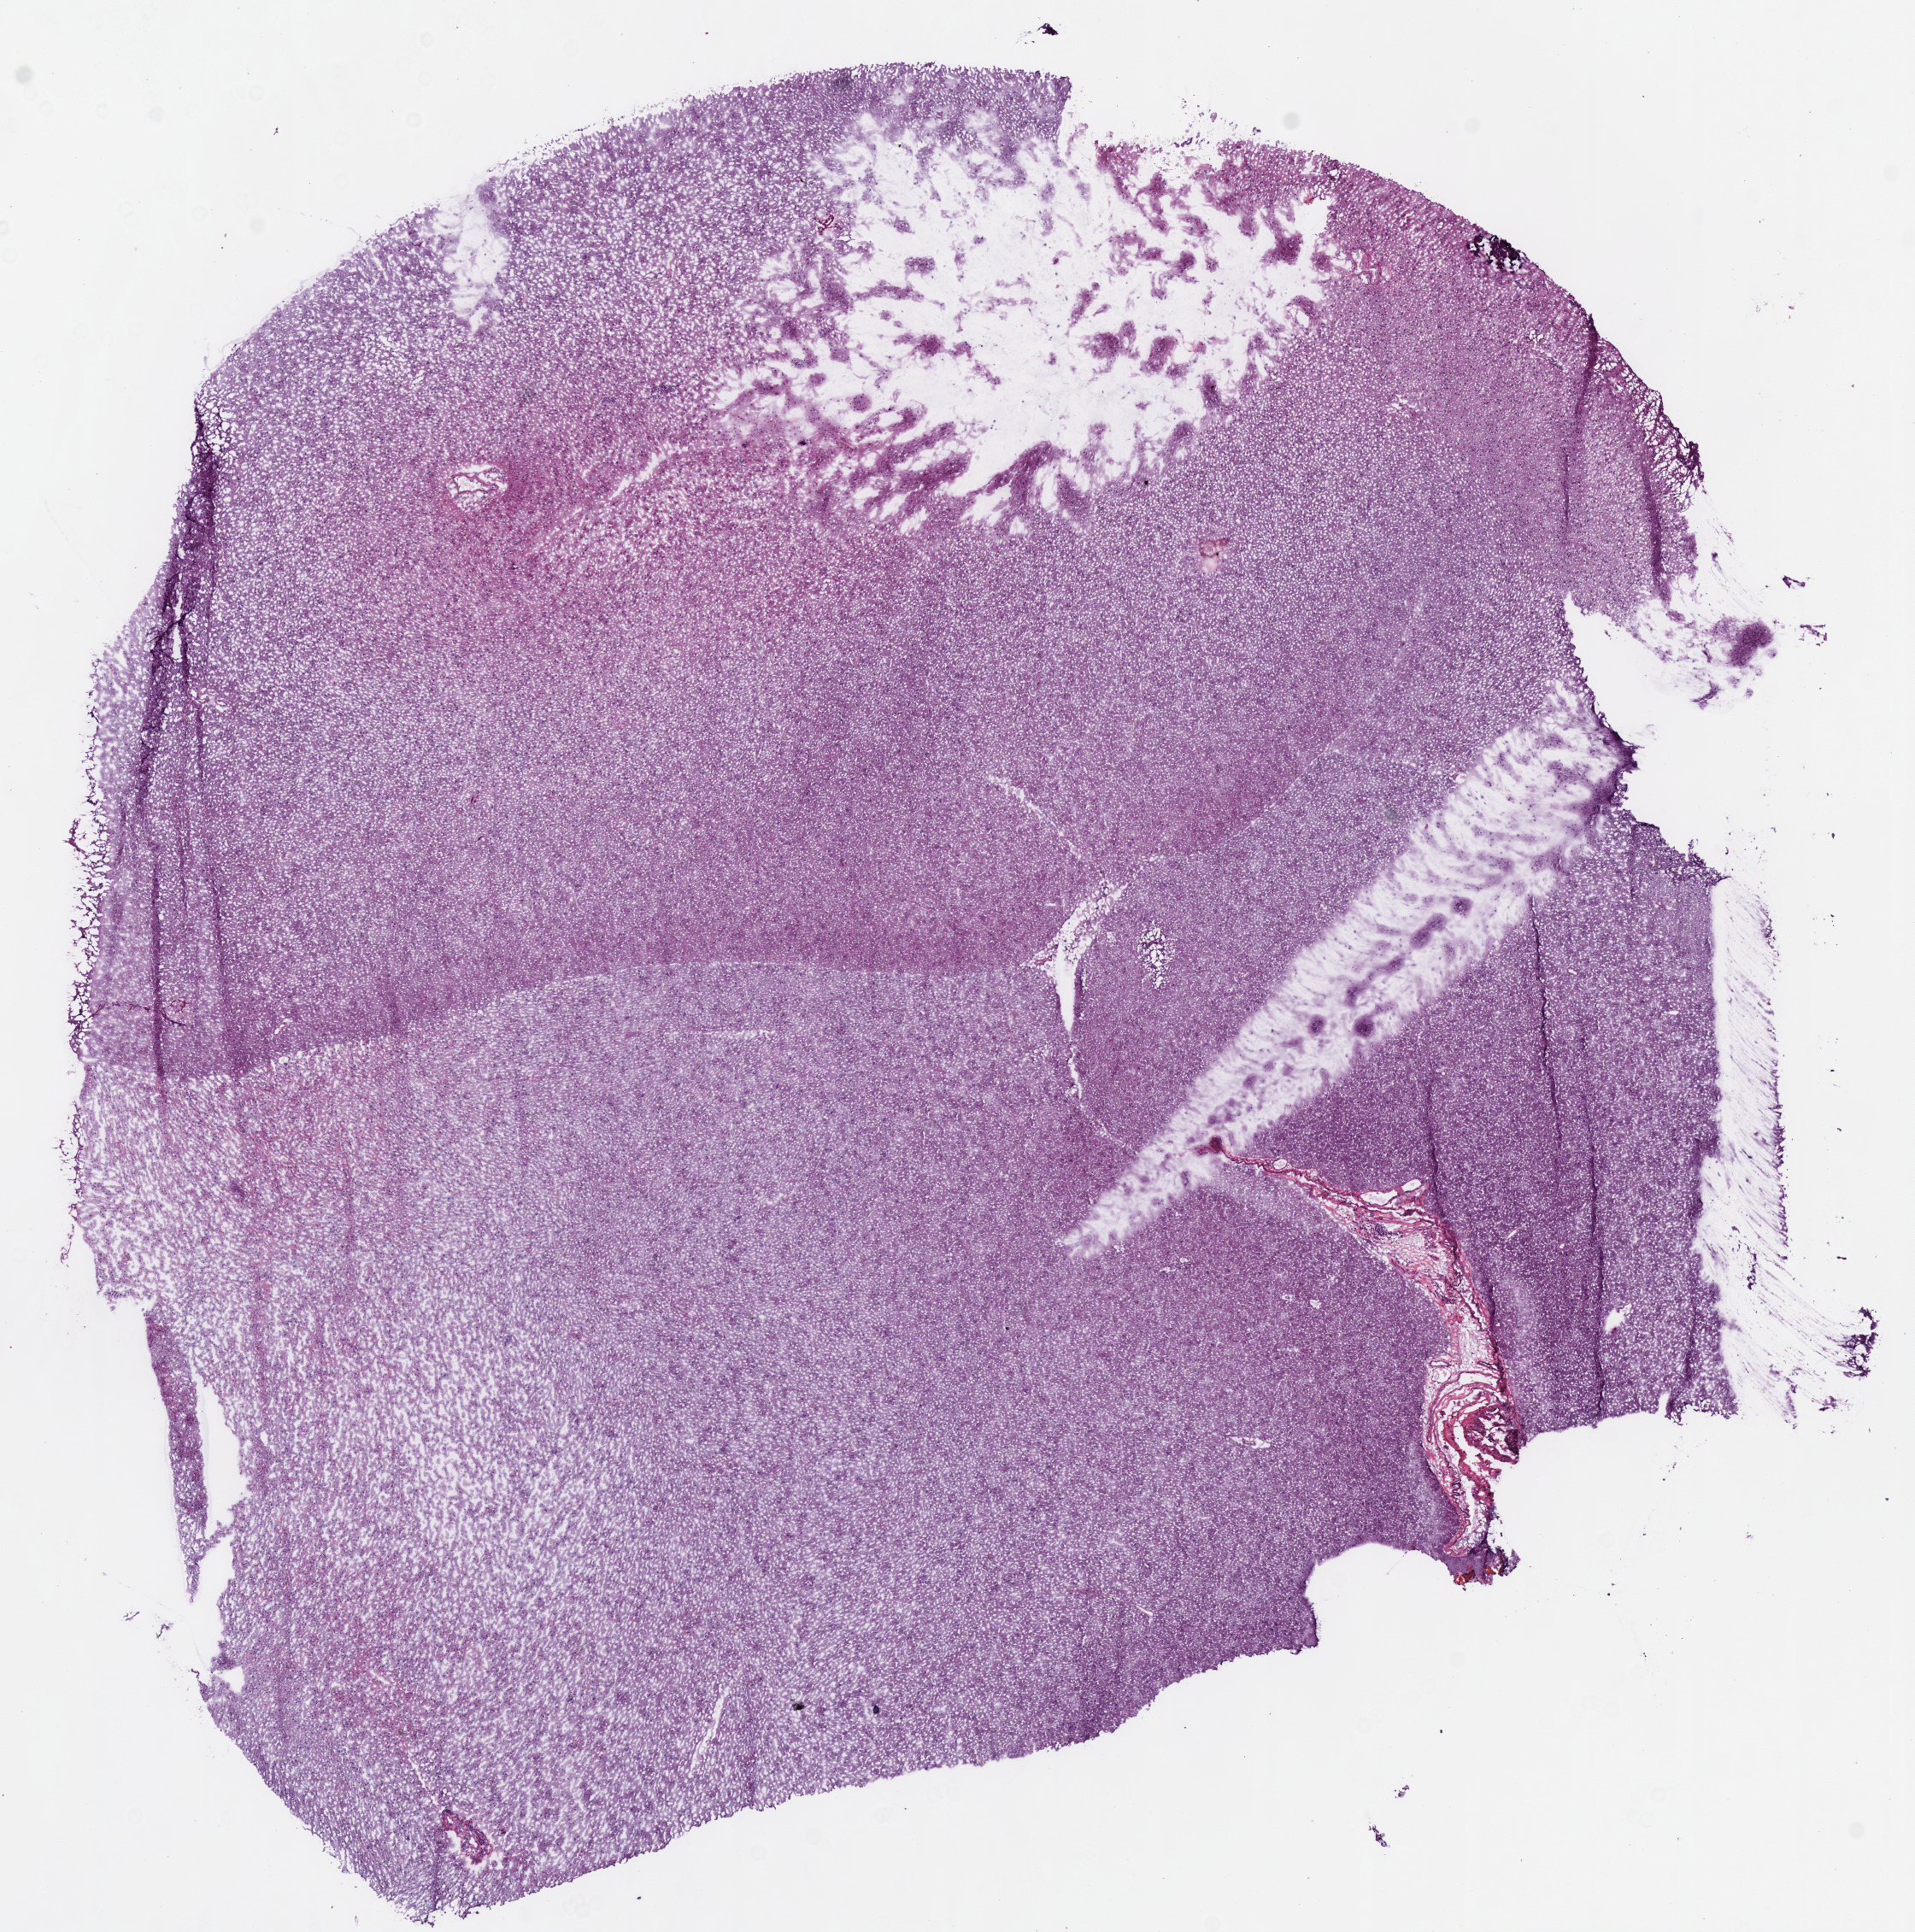
H&E whole-slide image, low-resolution overview of the scanned area, about 8.8 x 8.9 mm (acquisition: 40x scan), frozen section from the bottom of the tissue portion, sample: primary tumour, brain. Female, age 29 years at initial diagnosis.
Pathologic diagnosis: Mixed glioma.